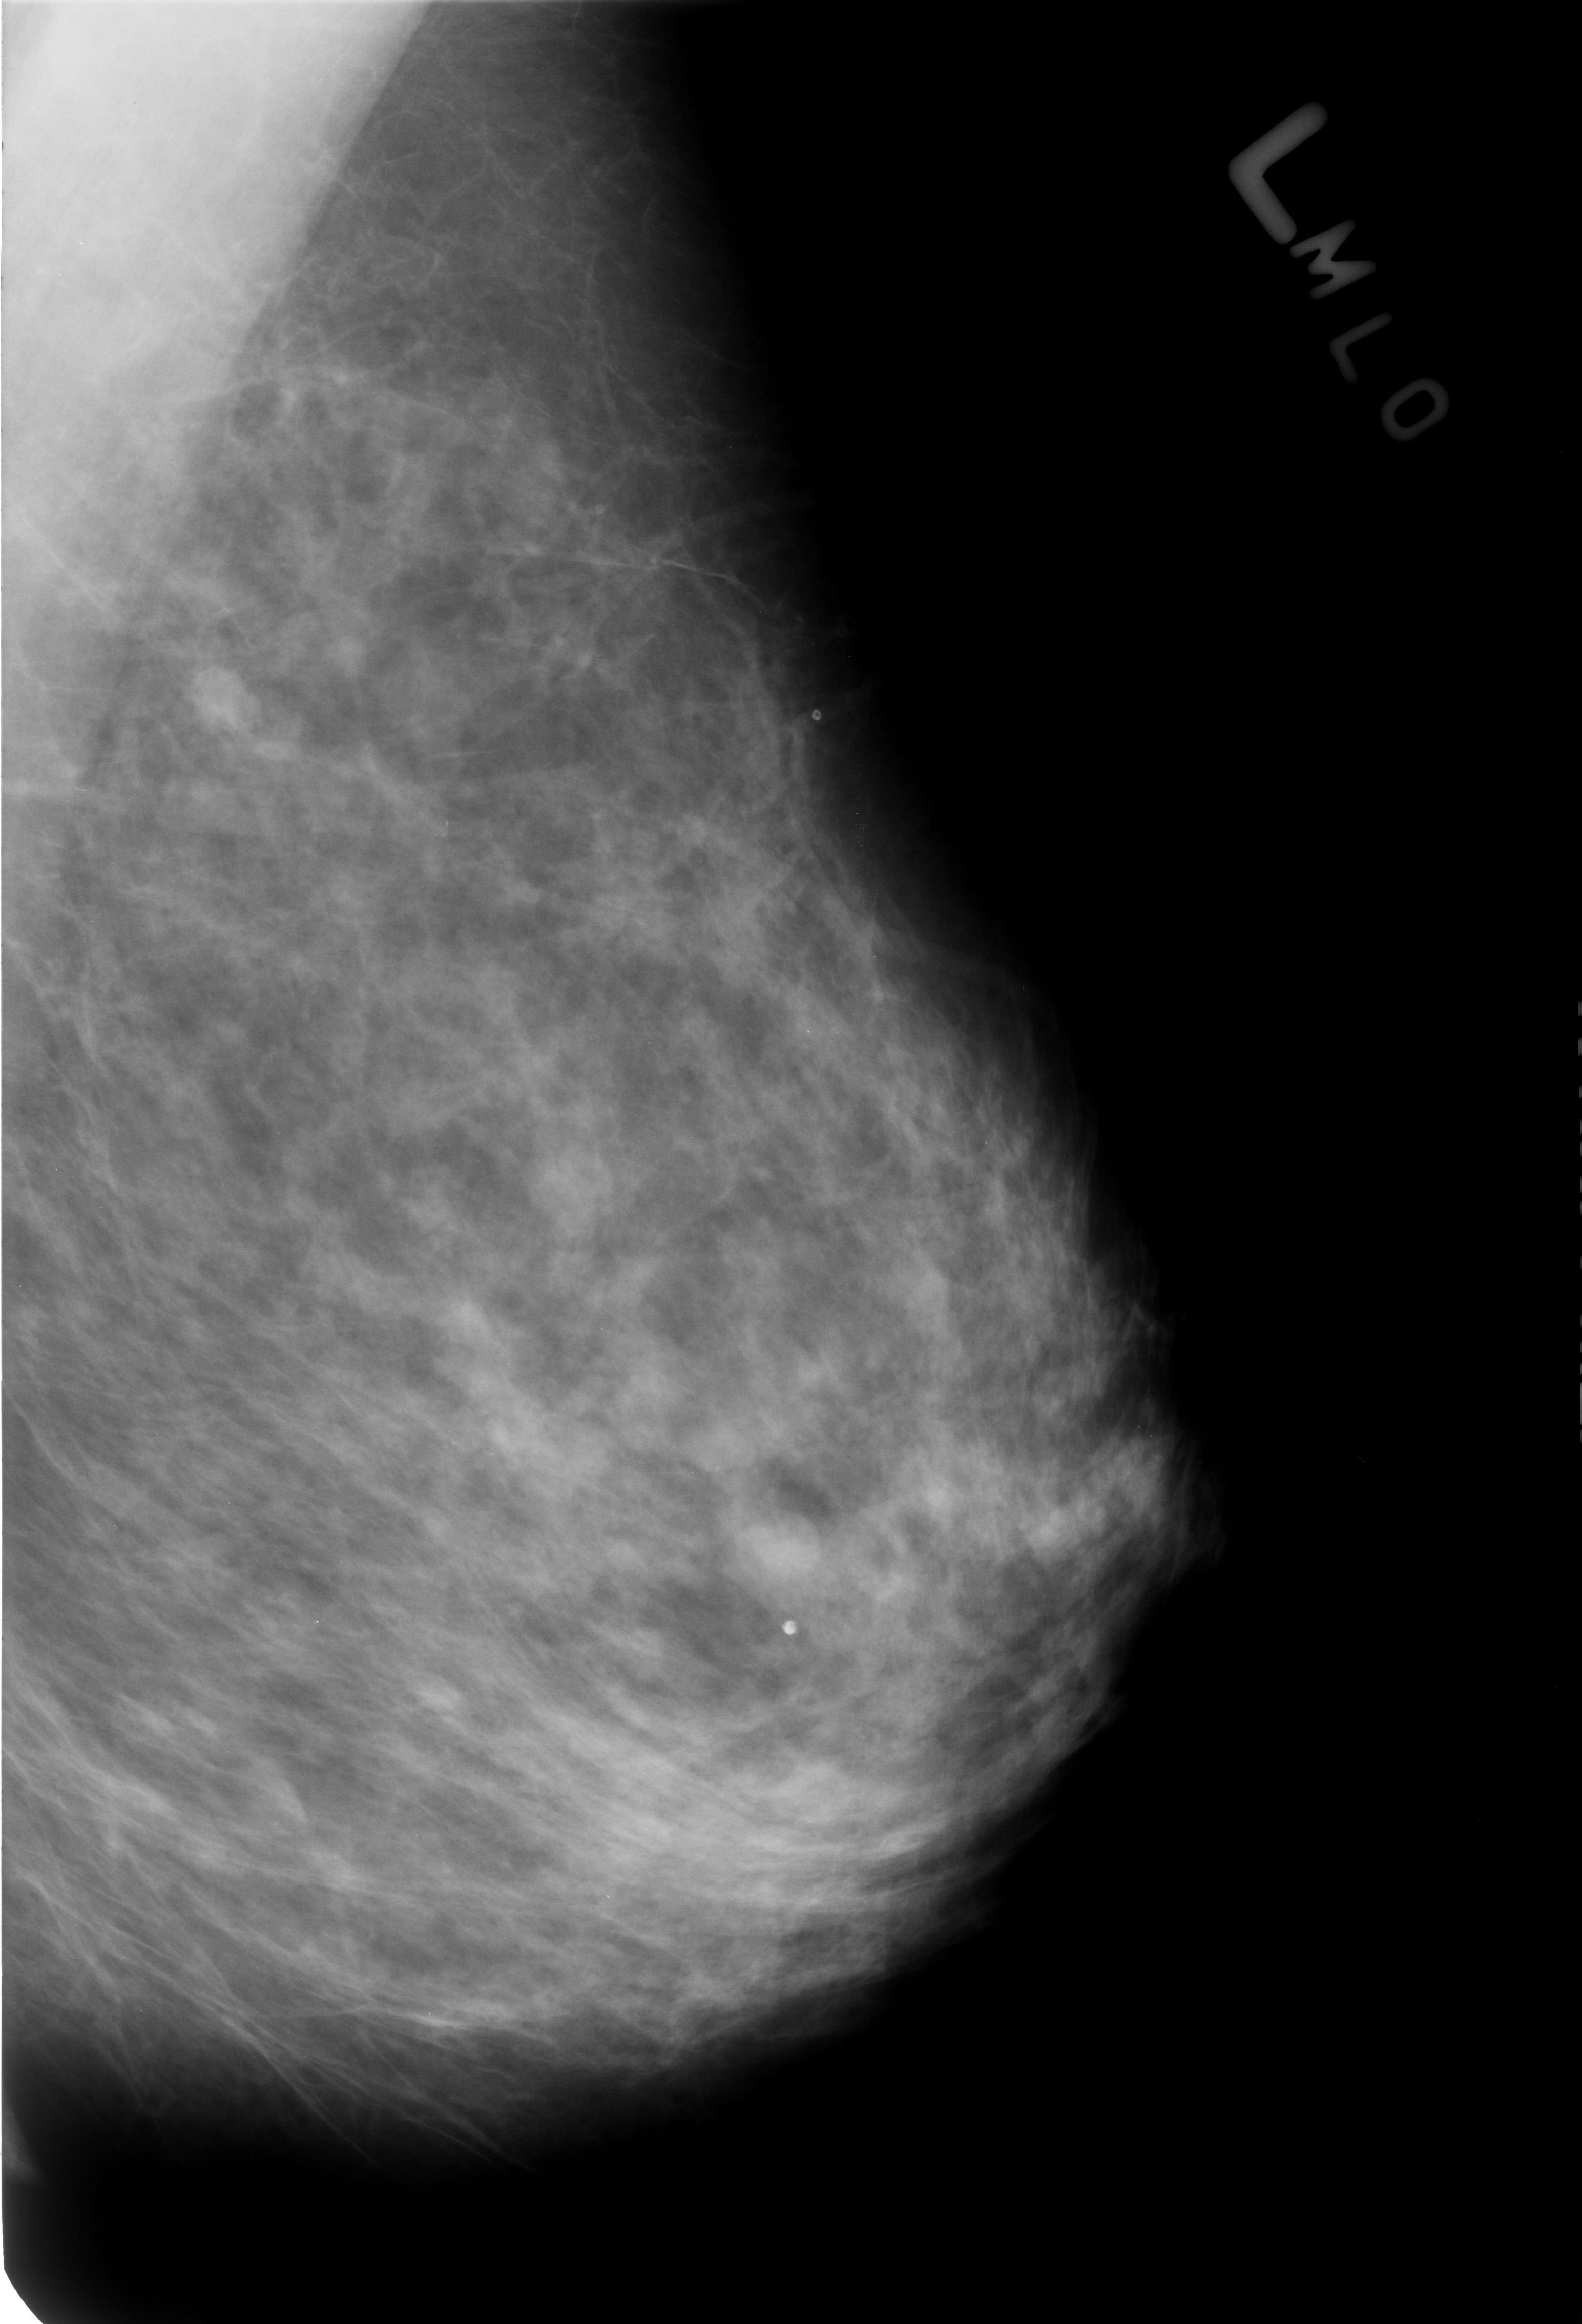
Digitized screen-film mammogram. Left breast. Mediolateral oblique (MLO) view. 1582 × 2324 image matrix.
Expert-marked regions of interest on this film, with their recorded descriptors:
- Finding 1 of 2: calcifications, morphology coarse / round and regular / lucent center; BI-RADS assessment category 2; benign; no additional work-up was recommended (outcome (as recorded, no biopsy): benign without callback): bounding box [x1, y1, x2, y2] px = [778, 1614, 800, 1636]
- Finding 2 of 2: calcifications, morphology coarse / round and regular / lucent center; BI-RADS assessment category 2; outcome (as recorded, no biopsy): benign without callback (not worked up further): [811, 696, 833, 722]